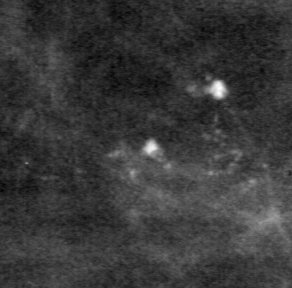
Crop from a digitized film mammogram around one marked abnormality, left breast, CC view.
- Marked abnormality: calcifications, morphology pleomorphic, distribution clustered; BI-RADS assessment category 4; subtlety rating 2 on a 1 (subtle) to 5 (obvious) scale; pathology (as recorded): benign.